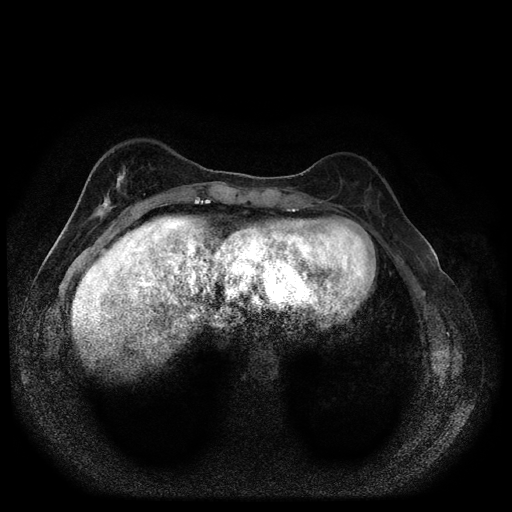
Breast MRI (dynamic contrast-enhanced, multi-phase), one axial slice. Position 30 of 116 along the scan axis. Dynamic contrast-enhanced series, time point 2 of 5 at this slice position (early post-contrast). 1.5 T. TE 2.7 ms, TR 5.4 ms. 2 mm slice thickness. 512 × 512 image matrix, field of view 330 × 330 mm. Female patient, age 49 years.
Annotated regions visible in this slice (semi-automatically segmented with operator editing):
- breast lesion (labelled 'tumour' in the annotation; benign lesions carry a separate 'benign' label): box from (x=85, y=163) to (x=129, y=227) px